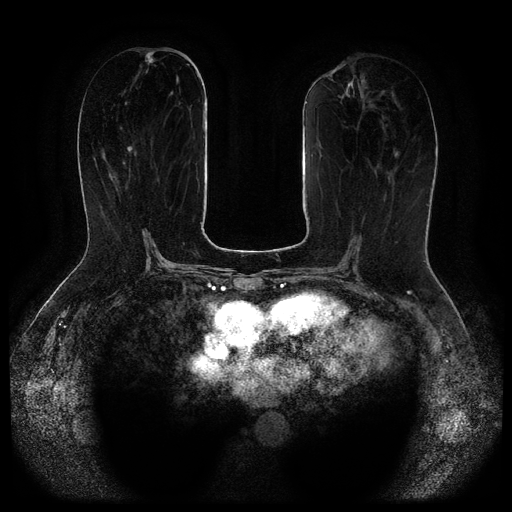
Breast MRI (dynamic contrast-enhanced, multi-phase), one axial slice; position 42 of 116 along the scan axis; dynamic contrast-enhanced series, time point 2 of 5 at this slice position (early post-contrast); 1.5 T; TE 2.6 ms, TR 5.3 ms; 2.1 mm slice thickness; 512 × 512 image matrix, field of view 360 × 360 mm. Patient: female, 65 years.
Annotated regions visible in this slice (semi-automatically segmented with operator editing):
- breast lesion (labelled 'tumour' in the annotation; benign lesions carry a separate 'benign' label): box from (x=145, y=52) to (x=154, y=65) px